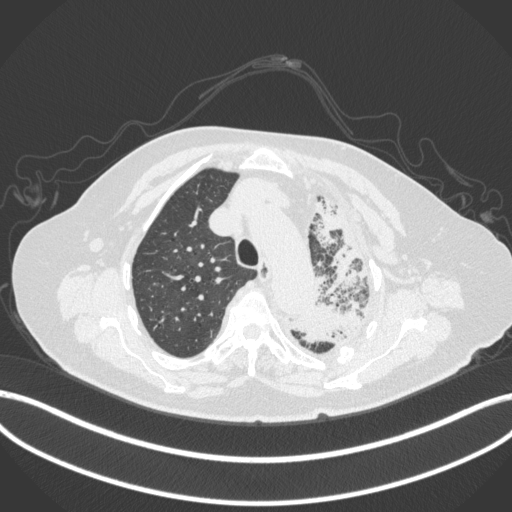
Chest CT, one axial slice; position 301 of 399 along the scan axis; 120 kVp; lung window (W 1500 / L -600 HU); 512 × 512 image matrix. Patient: female, 75 years. Case-level facts recorded for this patient, not image findings: clinical TNM (as recorded): T3 N3 M1.
Structures marked on this image (rectangle marked by the reading radiologist):
- lung tumour (recorded histology: adenocarcinoma): bounding box (x1, y1, x2, y2) in pixels: (284, 197, 366, 352)